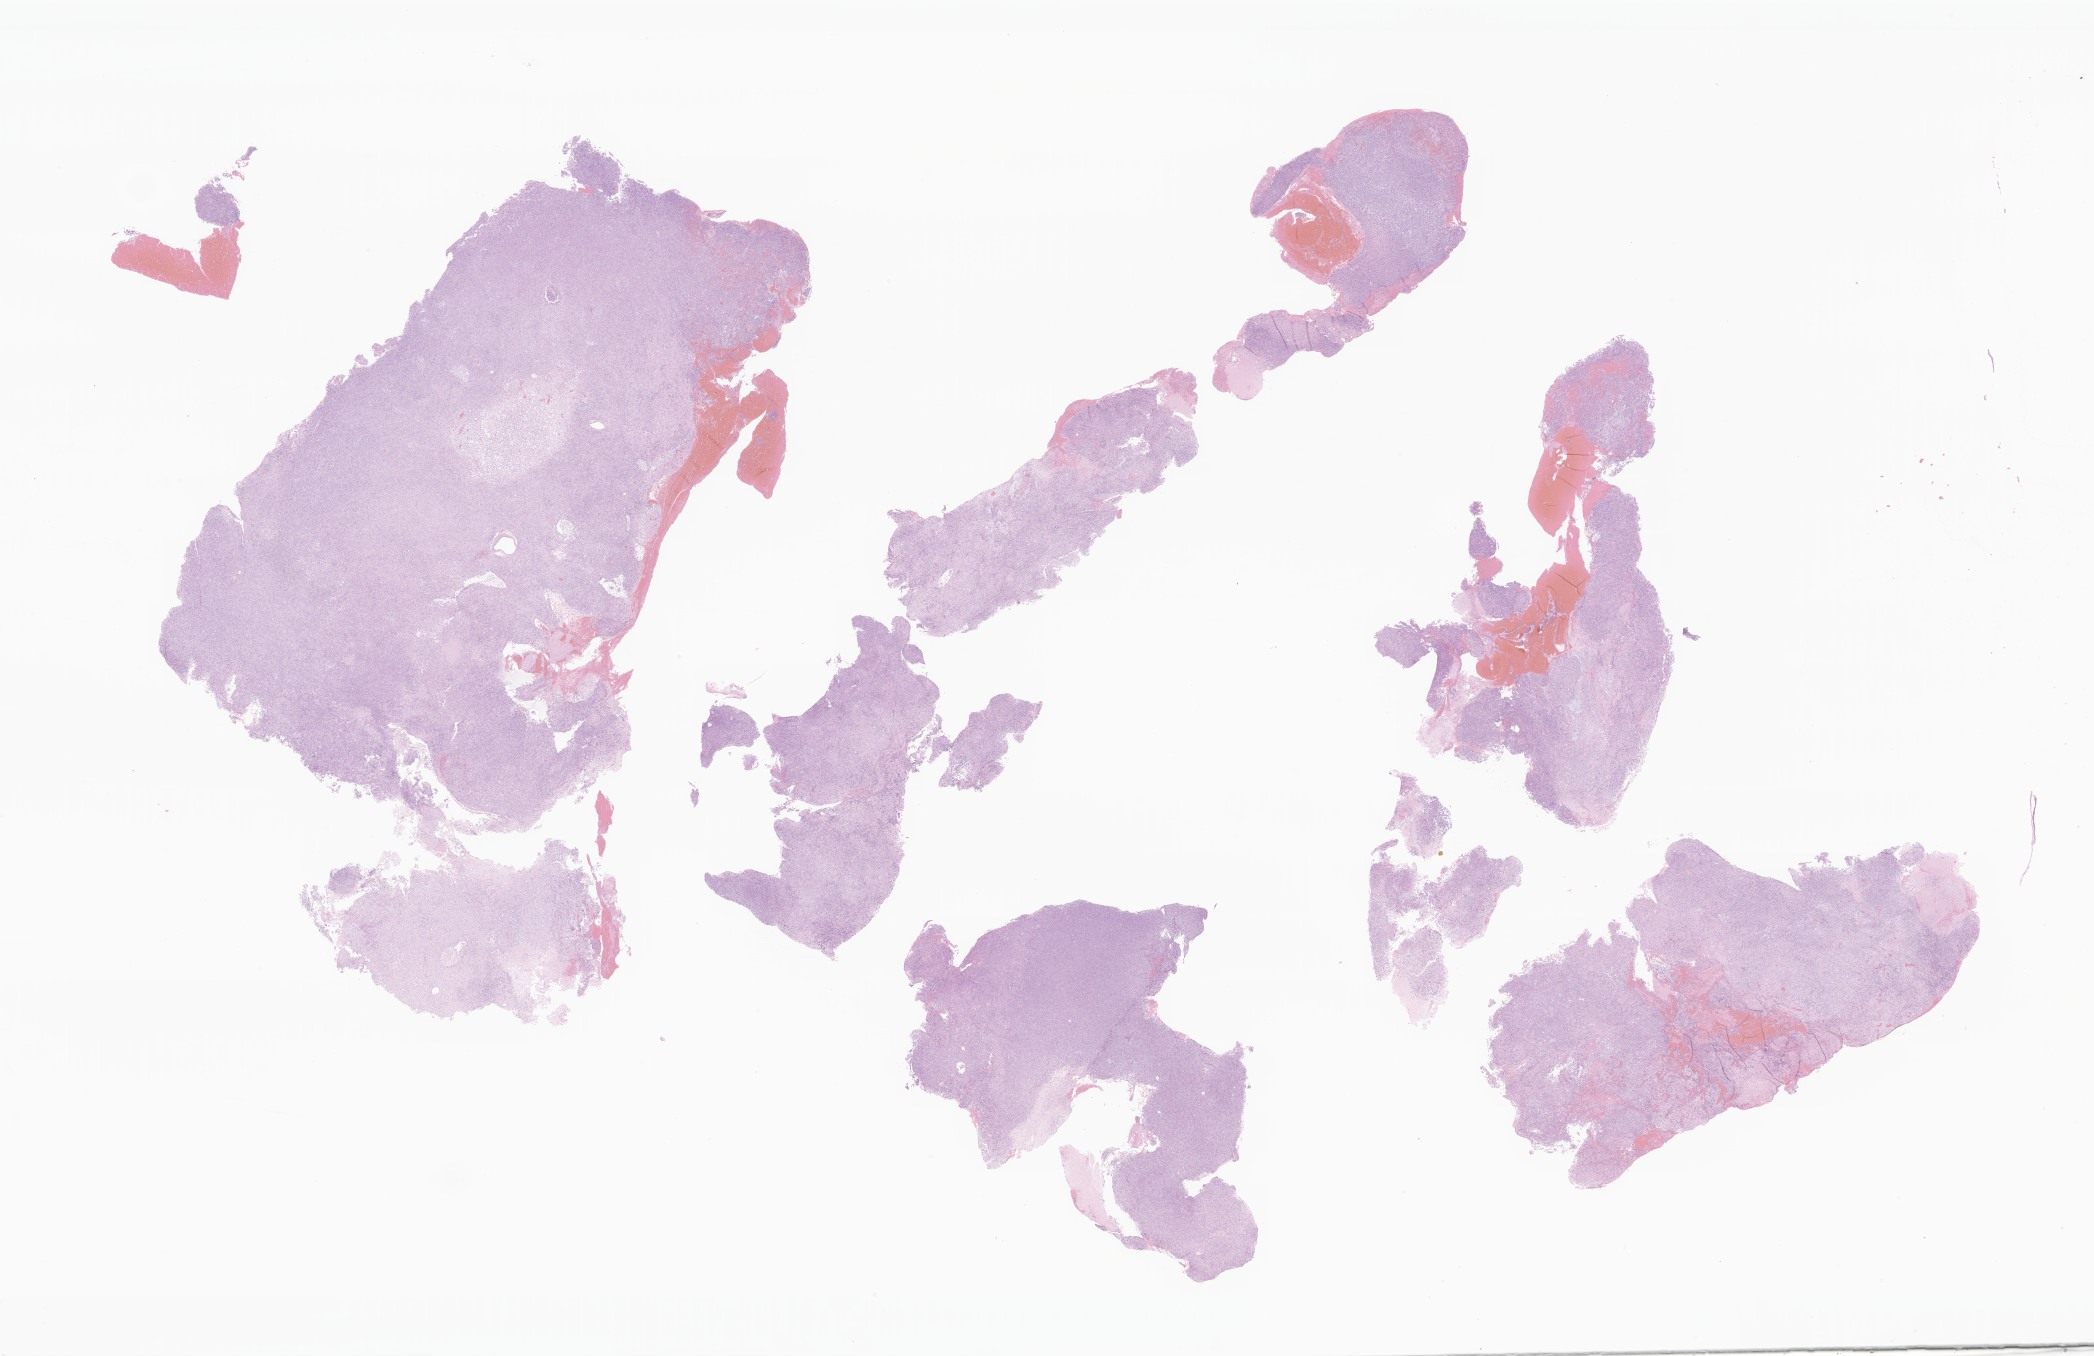
Digitized haematoxylin and eosin-stained section of tumor tissue from the brain — shown as a low-resolution overview of the whole scanned area (about 35.3 x 22.9 mm); formalin-fixed paraffin-embedded section. Female patient, age 389 days.
Recorded diagnosis: Atypical teratoid/rhabdoid tumor.